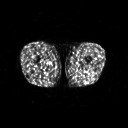
FDG PET of an extremity soft-tissue mass (from a PET/CT study), one axial slice. 128 × 128 image matrix, field of view 500 × 500 mm. Patient: male, 27 years. From the clinical record (not read from this slice): histological type: extraskeletal osteosarcoma; grade: high; site of the primary tumour: left adductur.
Structures marked on this image (expert contour drawn on MRI and transferred to this co-registered scan by the dataset authors):
- gross tumour volume (mass): box from (x=71, y=62) to (x=89, y=70) px